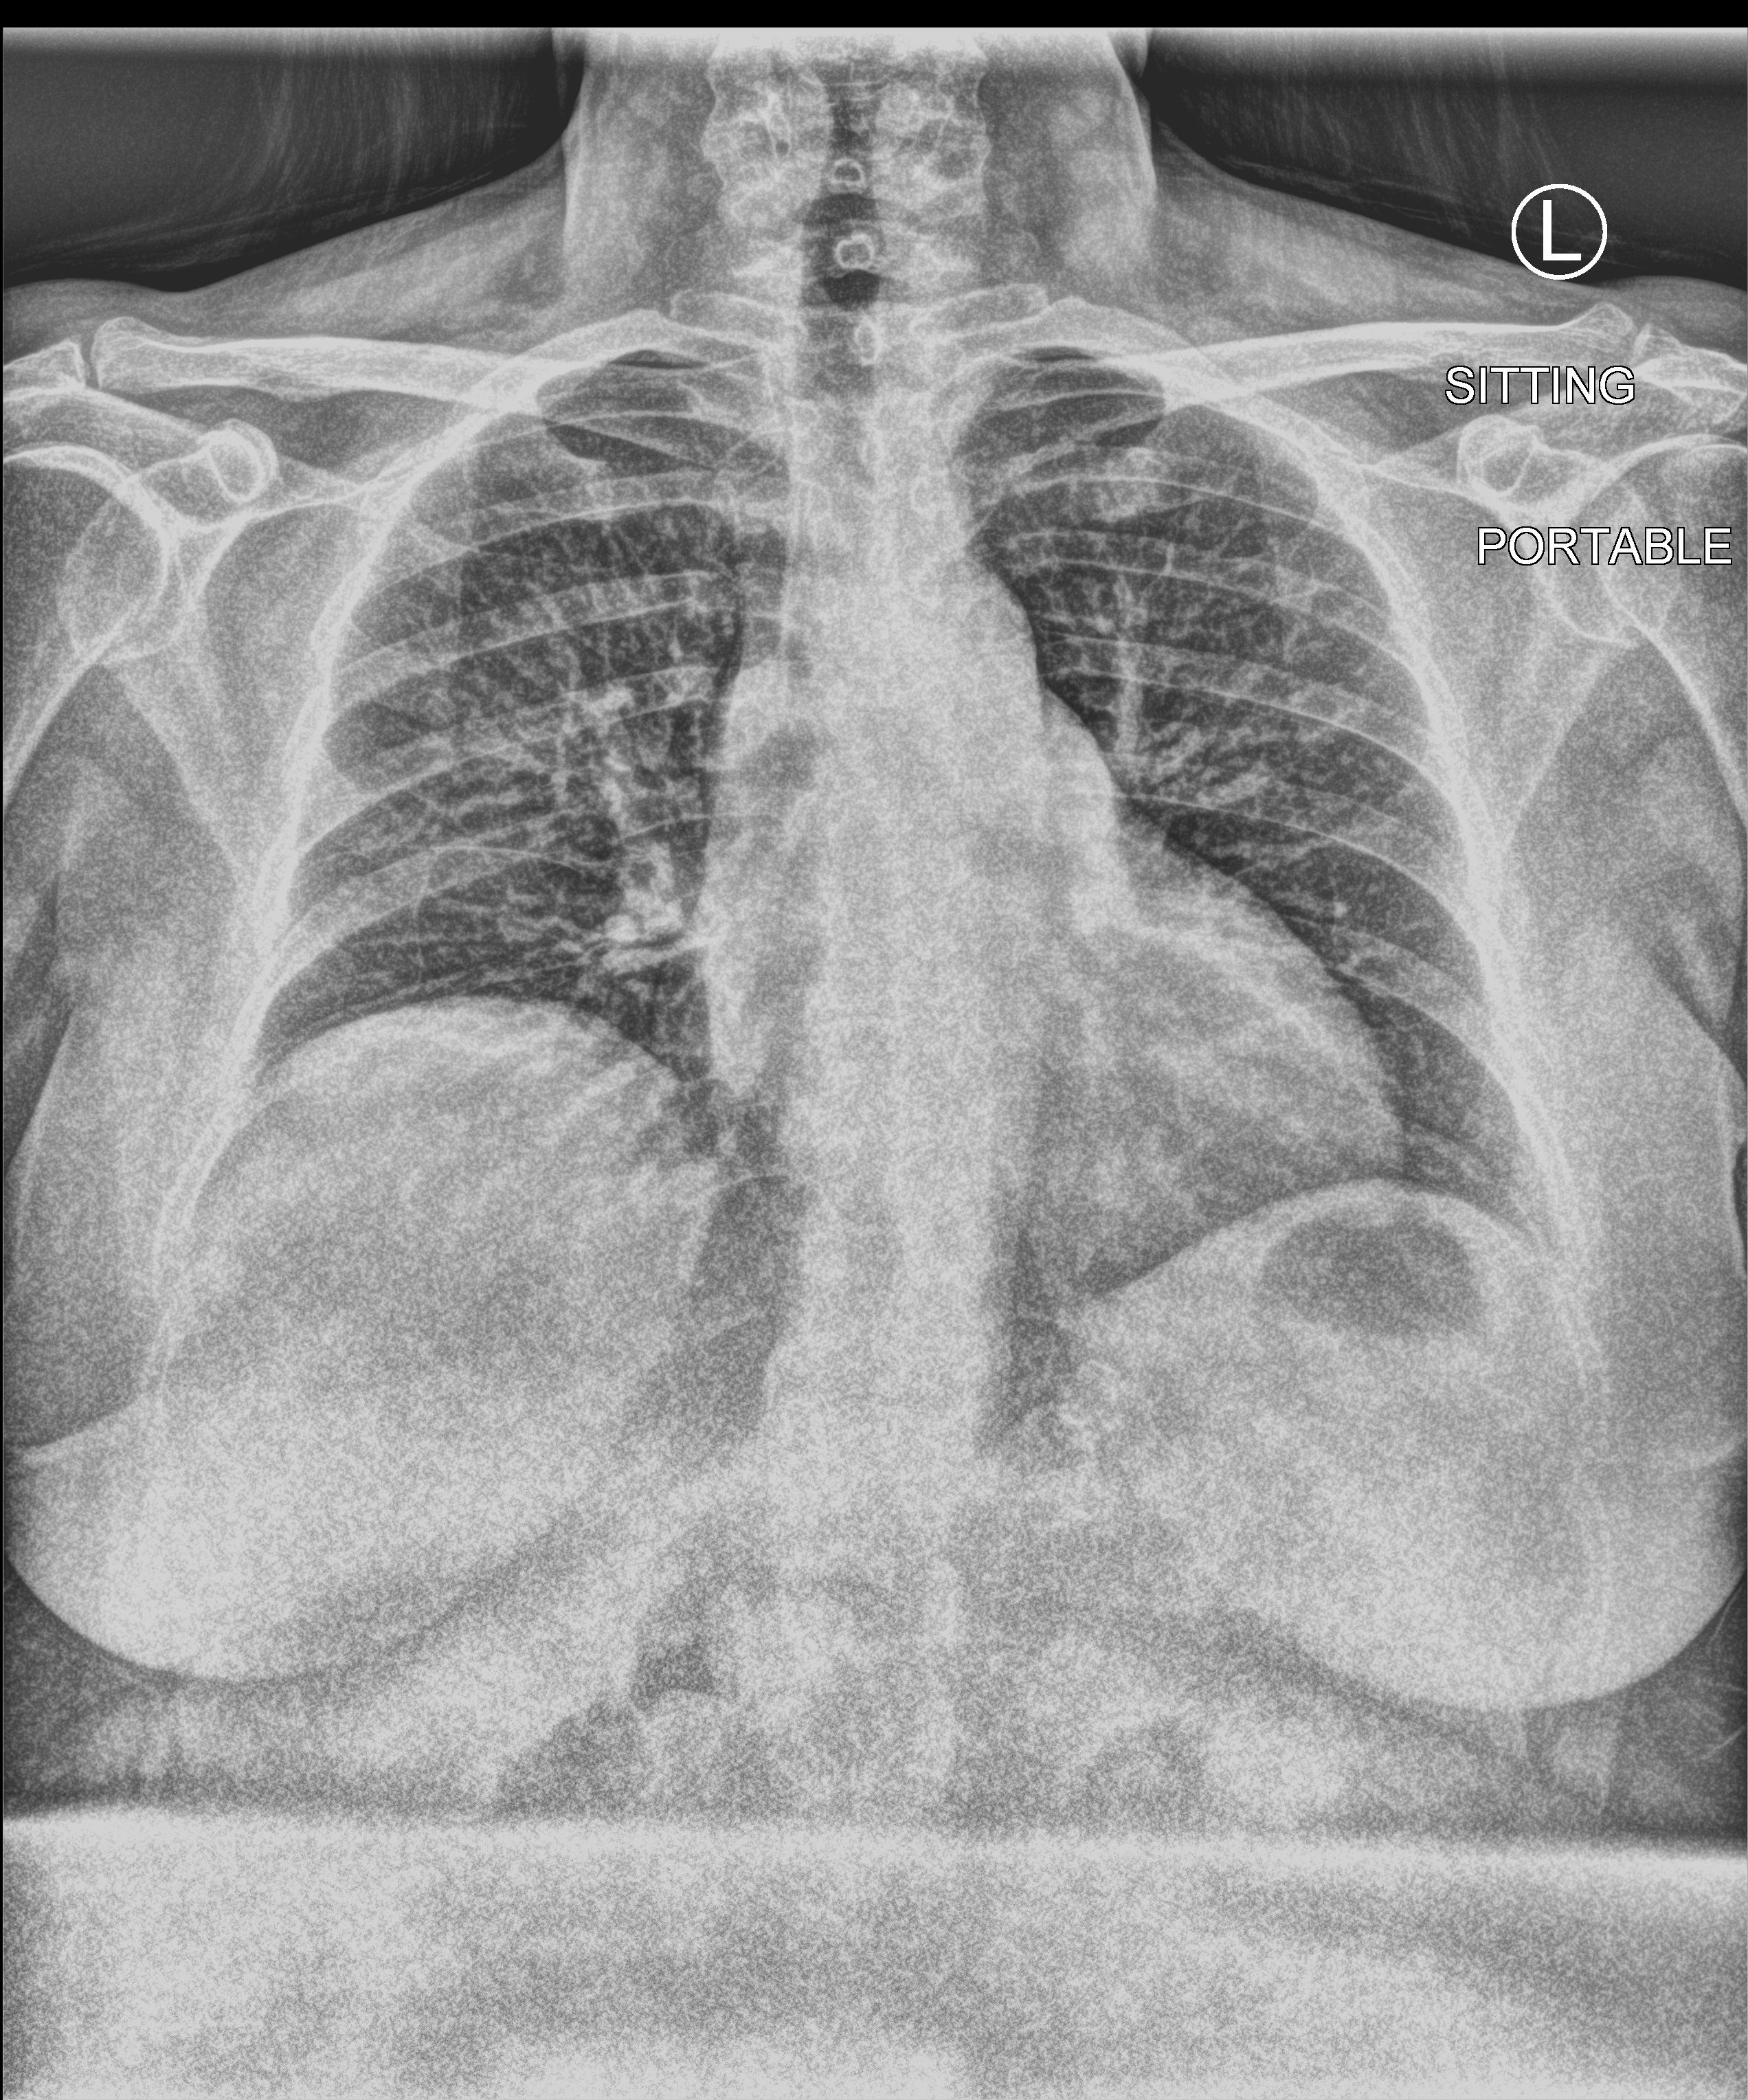
Chest X-ray (portable); anteroposterior (AP) projection. Patient hospitalised with COVID-19; female, aged 18–59 years.
From the hospital-stay record, not from the radiograph (when in the stay this image was taken is not recorded): mechanically ventilated during this hospital stay: no.